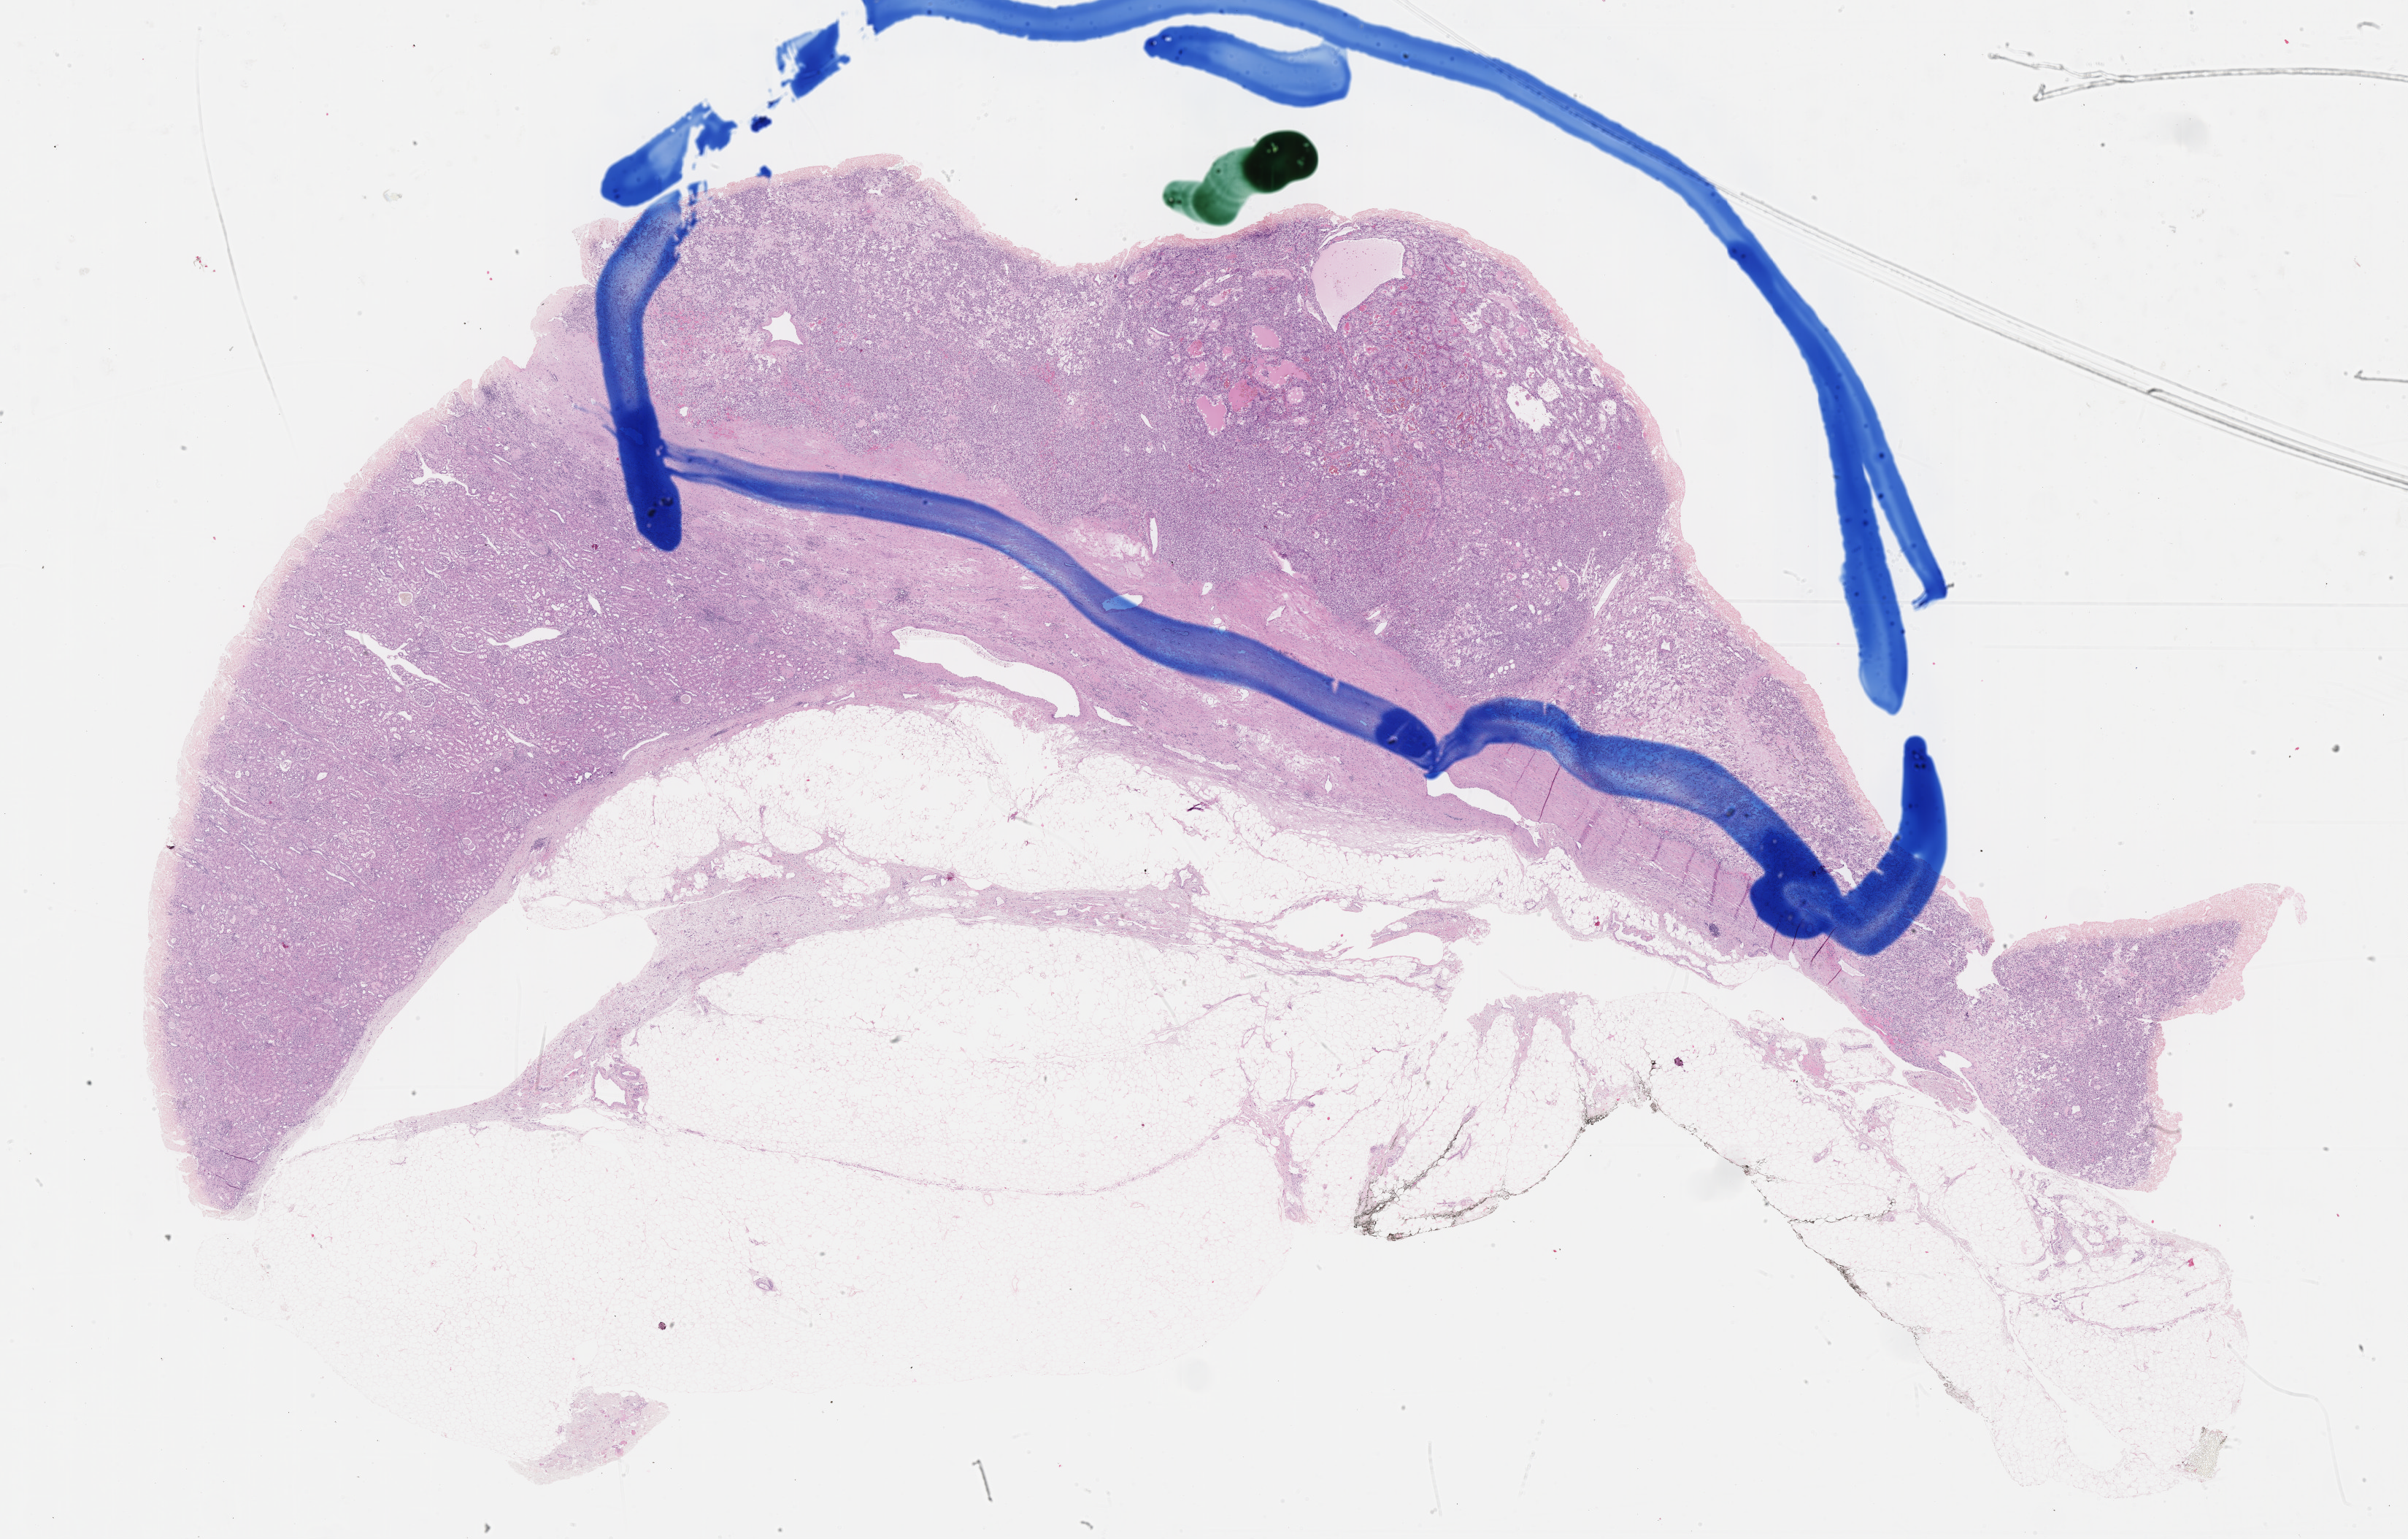
Whole-slide histology image, H&E, whole scanned area (about 26.7 x 17.0 mm) shown as a low-resolution overview. Formalin-fixed paraffin-embedded (FFPE) diagnostic section. Sample: primary tumour, kidney. Female patient; age at initial diagnosis 63 years. Histologic grade: G4 (undifferentiated).
* AJCC pathologic stage: I
* laterality: left
* histologic diagnosis: Clear cell adenocarcinoma, NOS